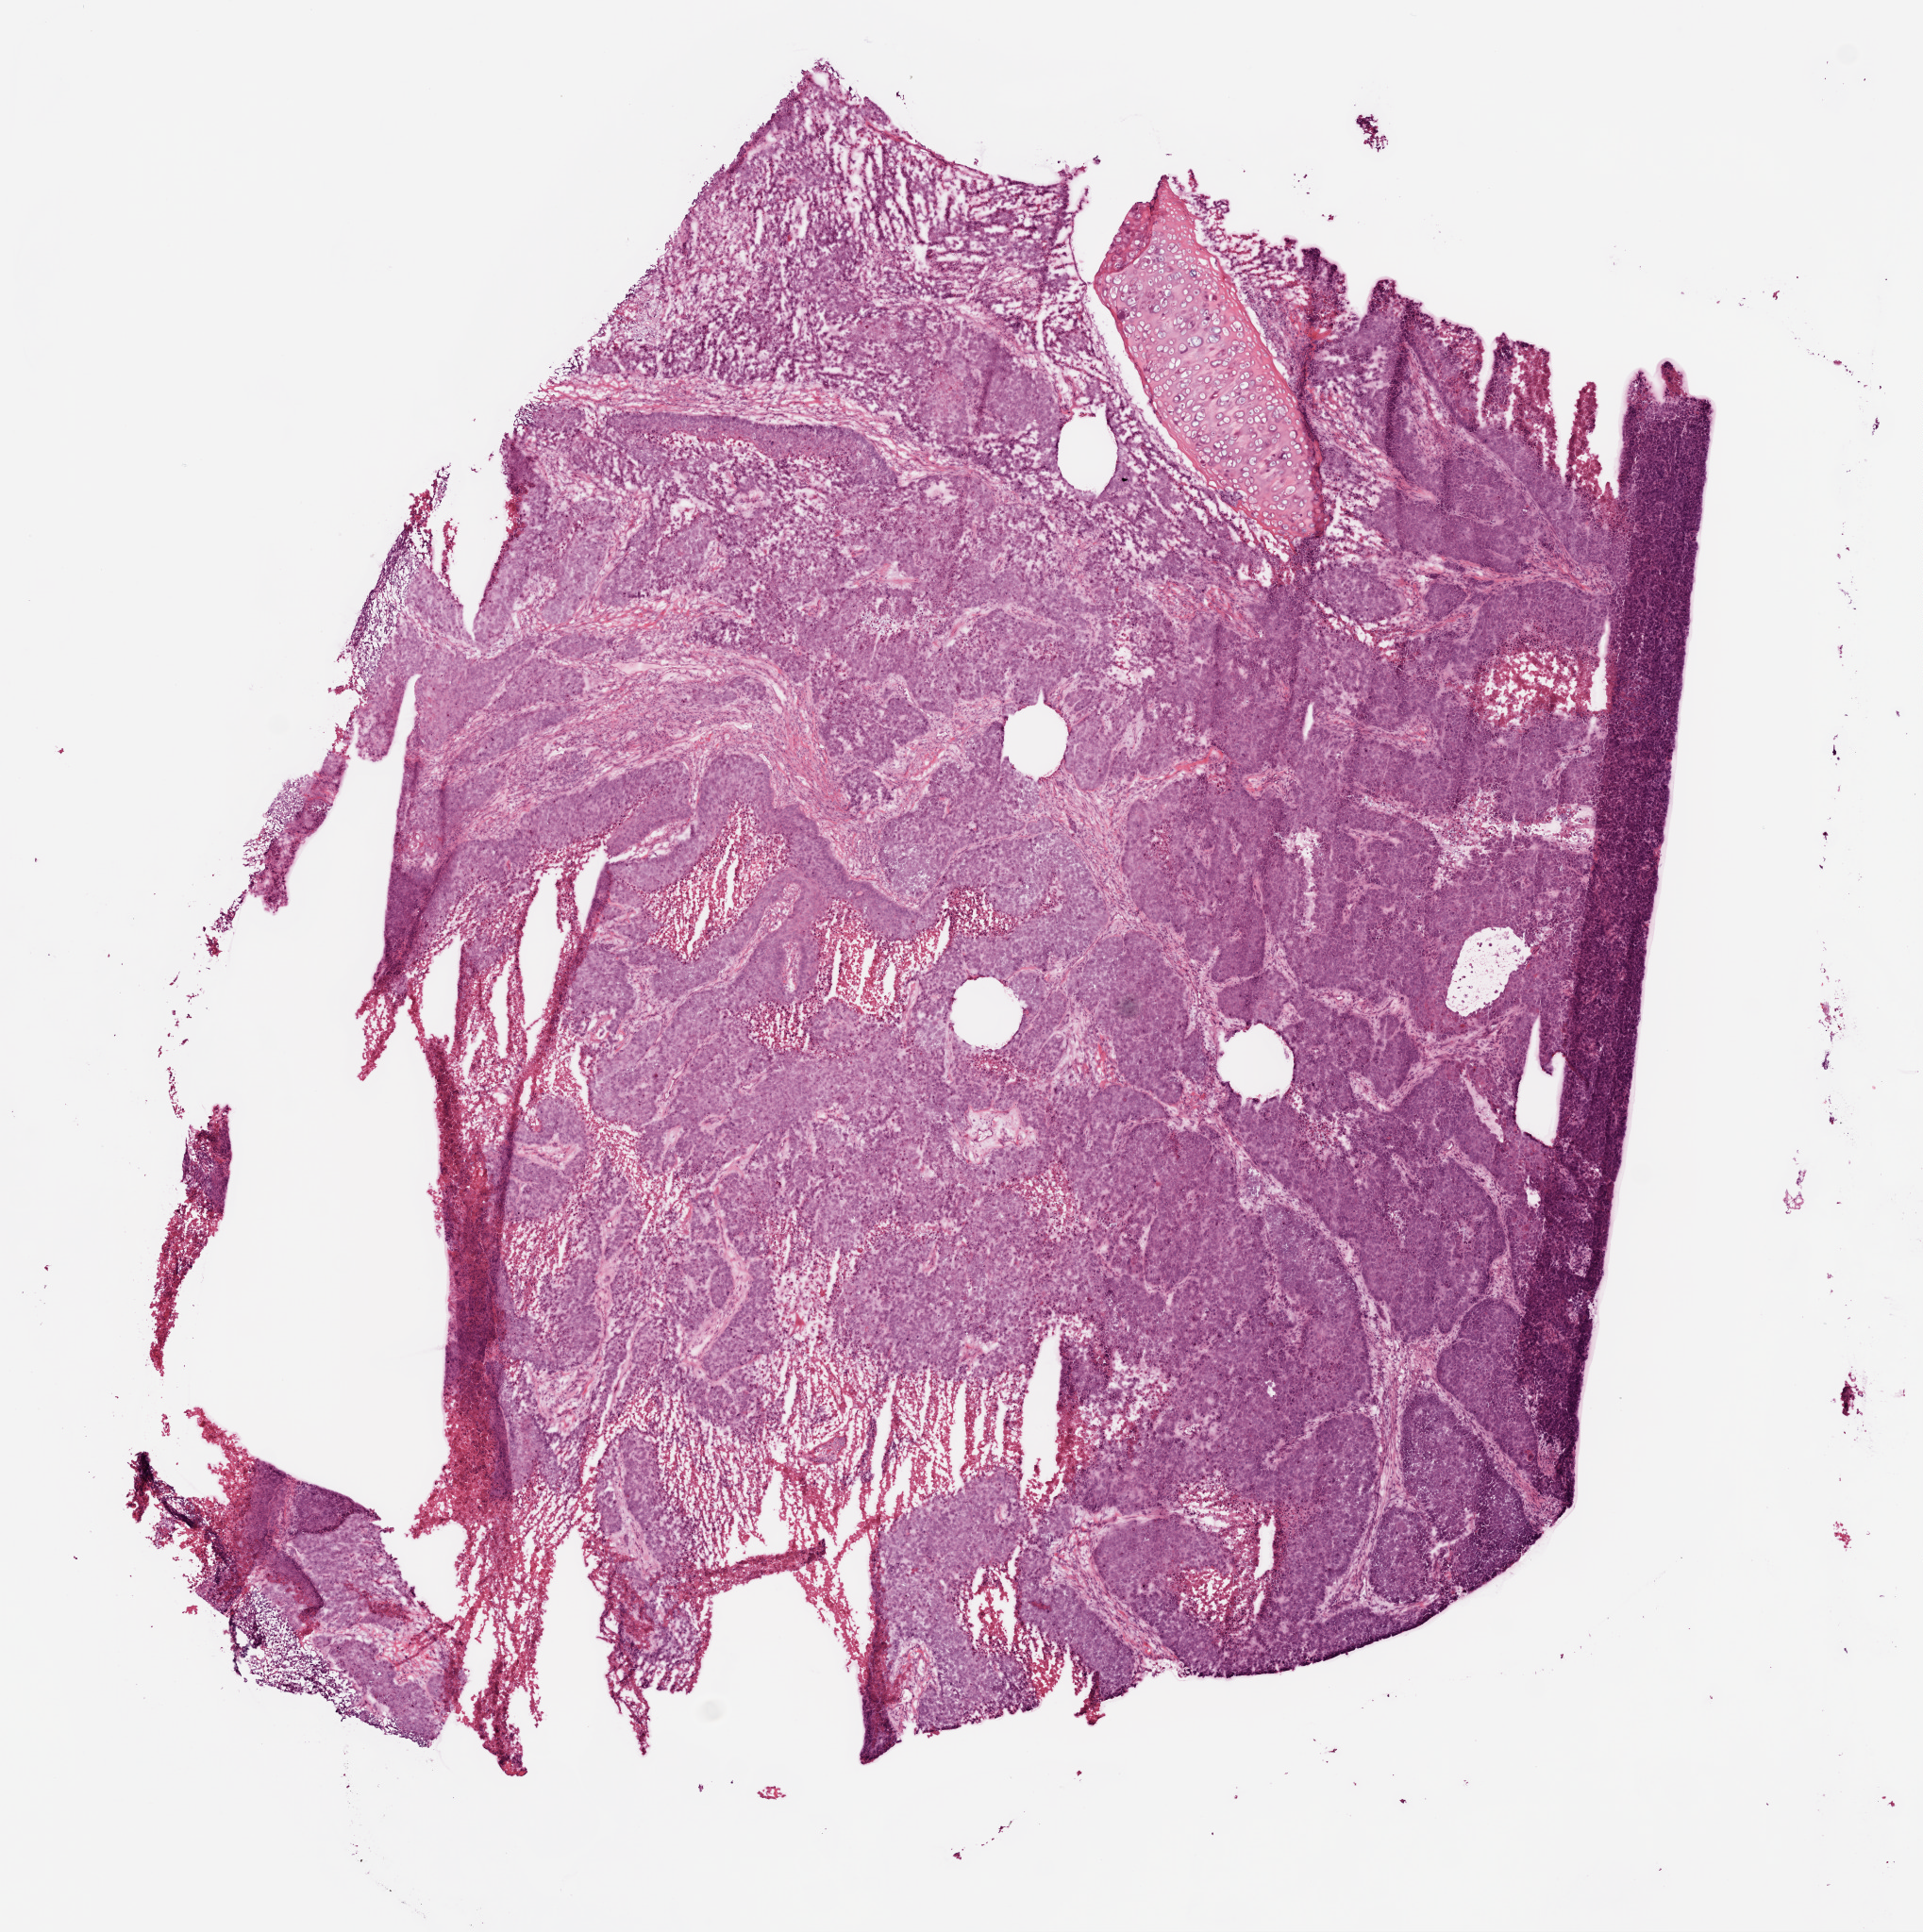
Digitized H&E-stained tissue section (whole slide), whole scanned area (about 8.2 x 8.3 mm) shown as a low-resolution overview. Frozen section from the top of the tissue portion. Lung, primary tumour sample. Patient: male, age at initial diagnosis 66 years. Composition of this section per pathologist review: tumour cells 80%, tumour nuclei 80%, normal cells 0%, stromal cells 10%, necrosis 10%.
AJCC pathologic stage: IIIA (7th edition). Diagnosis: Squamous cell carcinoma, NOS (overlapping lesion of lung).